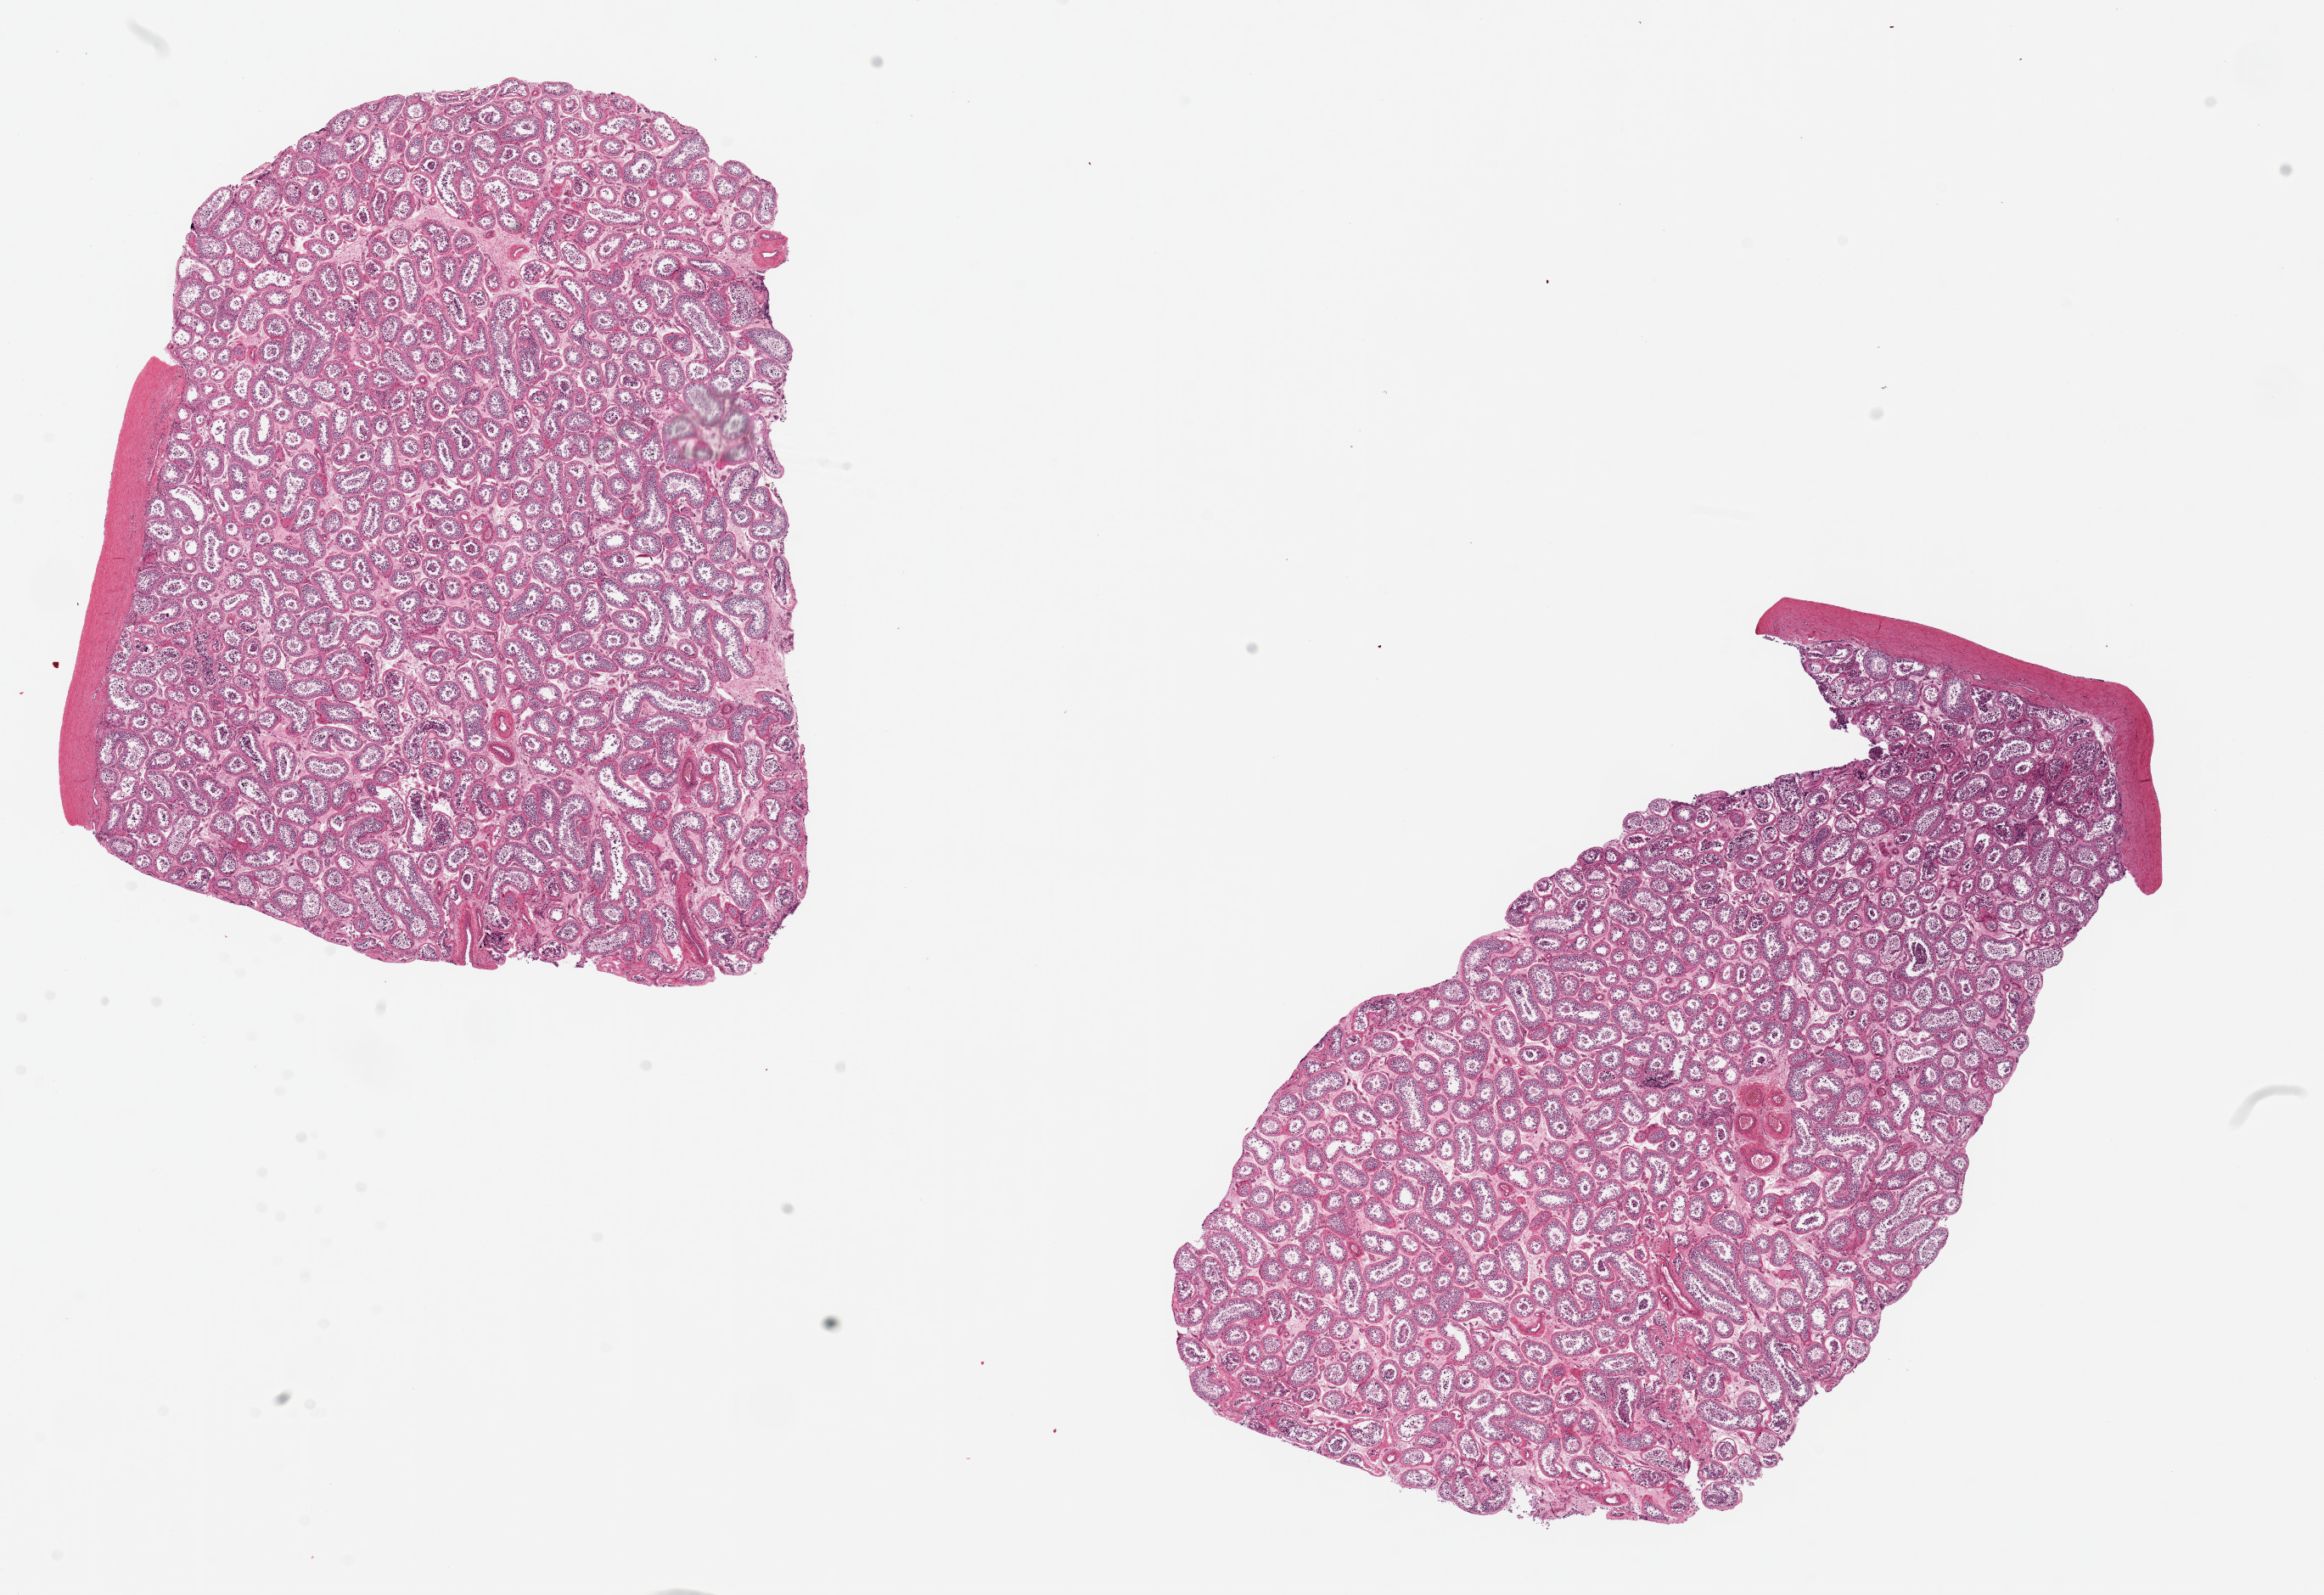
Hematoxylin and eosin (H&E) whole-slide image, shown as a low-resolution overview of the whole scanned area (about 21.7 x 14.9 mm, slide scanned at 20x). PAXgene-fixed paraffin-embedded (PFPE) section. Sampled site (target tissue): testis. Tissue donor sample. Donor: male.
Pathologist's review note for this sample: 2 pieces, 8x7 & 11x6mm; Capsule present along one side of each piece (should be excluded); slightly reduced spermatogenesis.